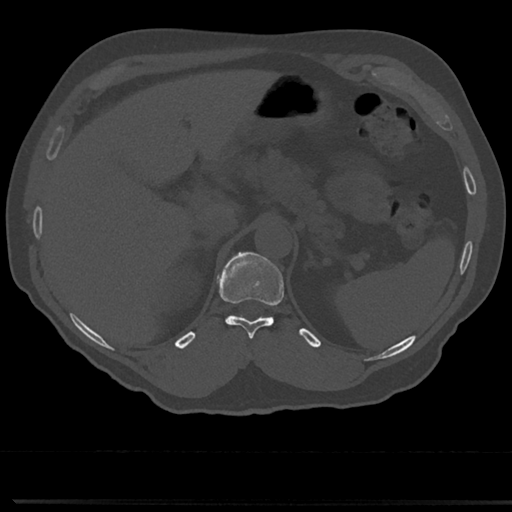
CT including the spine, one axial slice. Position 194 of 817 along the scan axis. Reconstruction kernel Br40s/3. 120 kVp. Bone window (W 1800 / L 400 HU). 512 × 512 image matrix, field of view 355 × 355 mm. Male patient, age 61 years. Case-level facts recorded for this patient, not image findings: primary cancer: prostate.
Structures marked on this image (semi-automatic segmentation, software-assisted and operator-edited):
- T11 vertebra: box from (x=220, y=255) to (x=284, y=340) px
- T12 vertebra: (x=222, y=253)–(x=250, y=279)